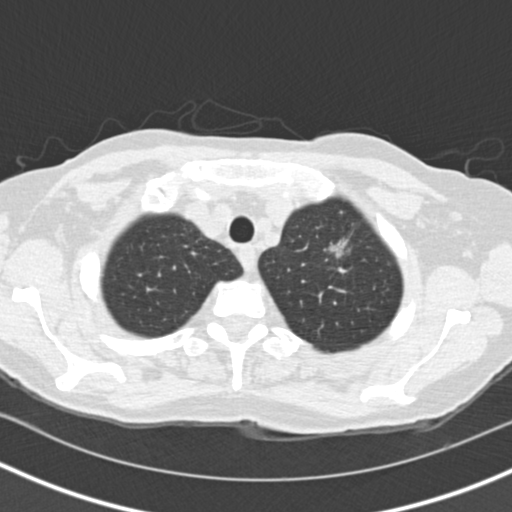
Low-dose screening chest CT, one axial slice; position 125 of 146 along the scan axis; reconstruction kernel B30f; lung window (W 1500 / L -600 HU); 2 mm slice thickness; 512 × 512 image matrix, field of view 310 × 310 mm.
Annotated regions visible in this slice (manually delineated by an expert):
- lesion 1 (tumor, upper lobe of left lung): box from (x=329, y=240) to (x=347, y=257) px